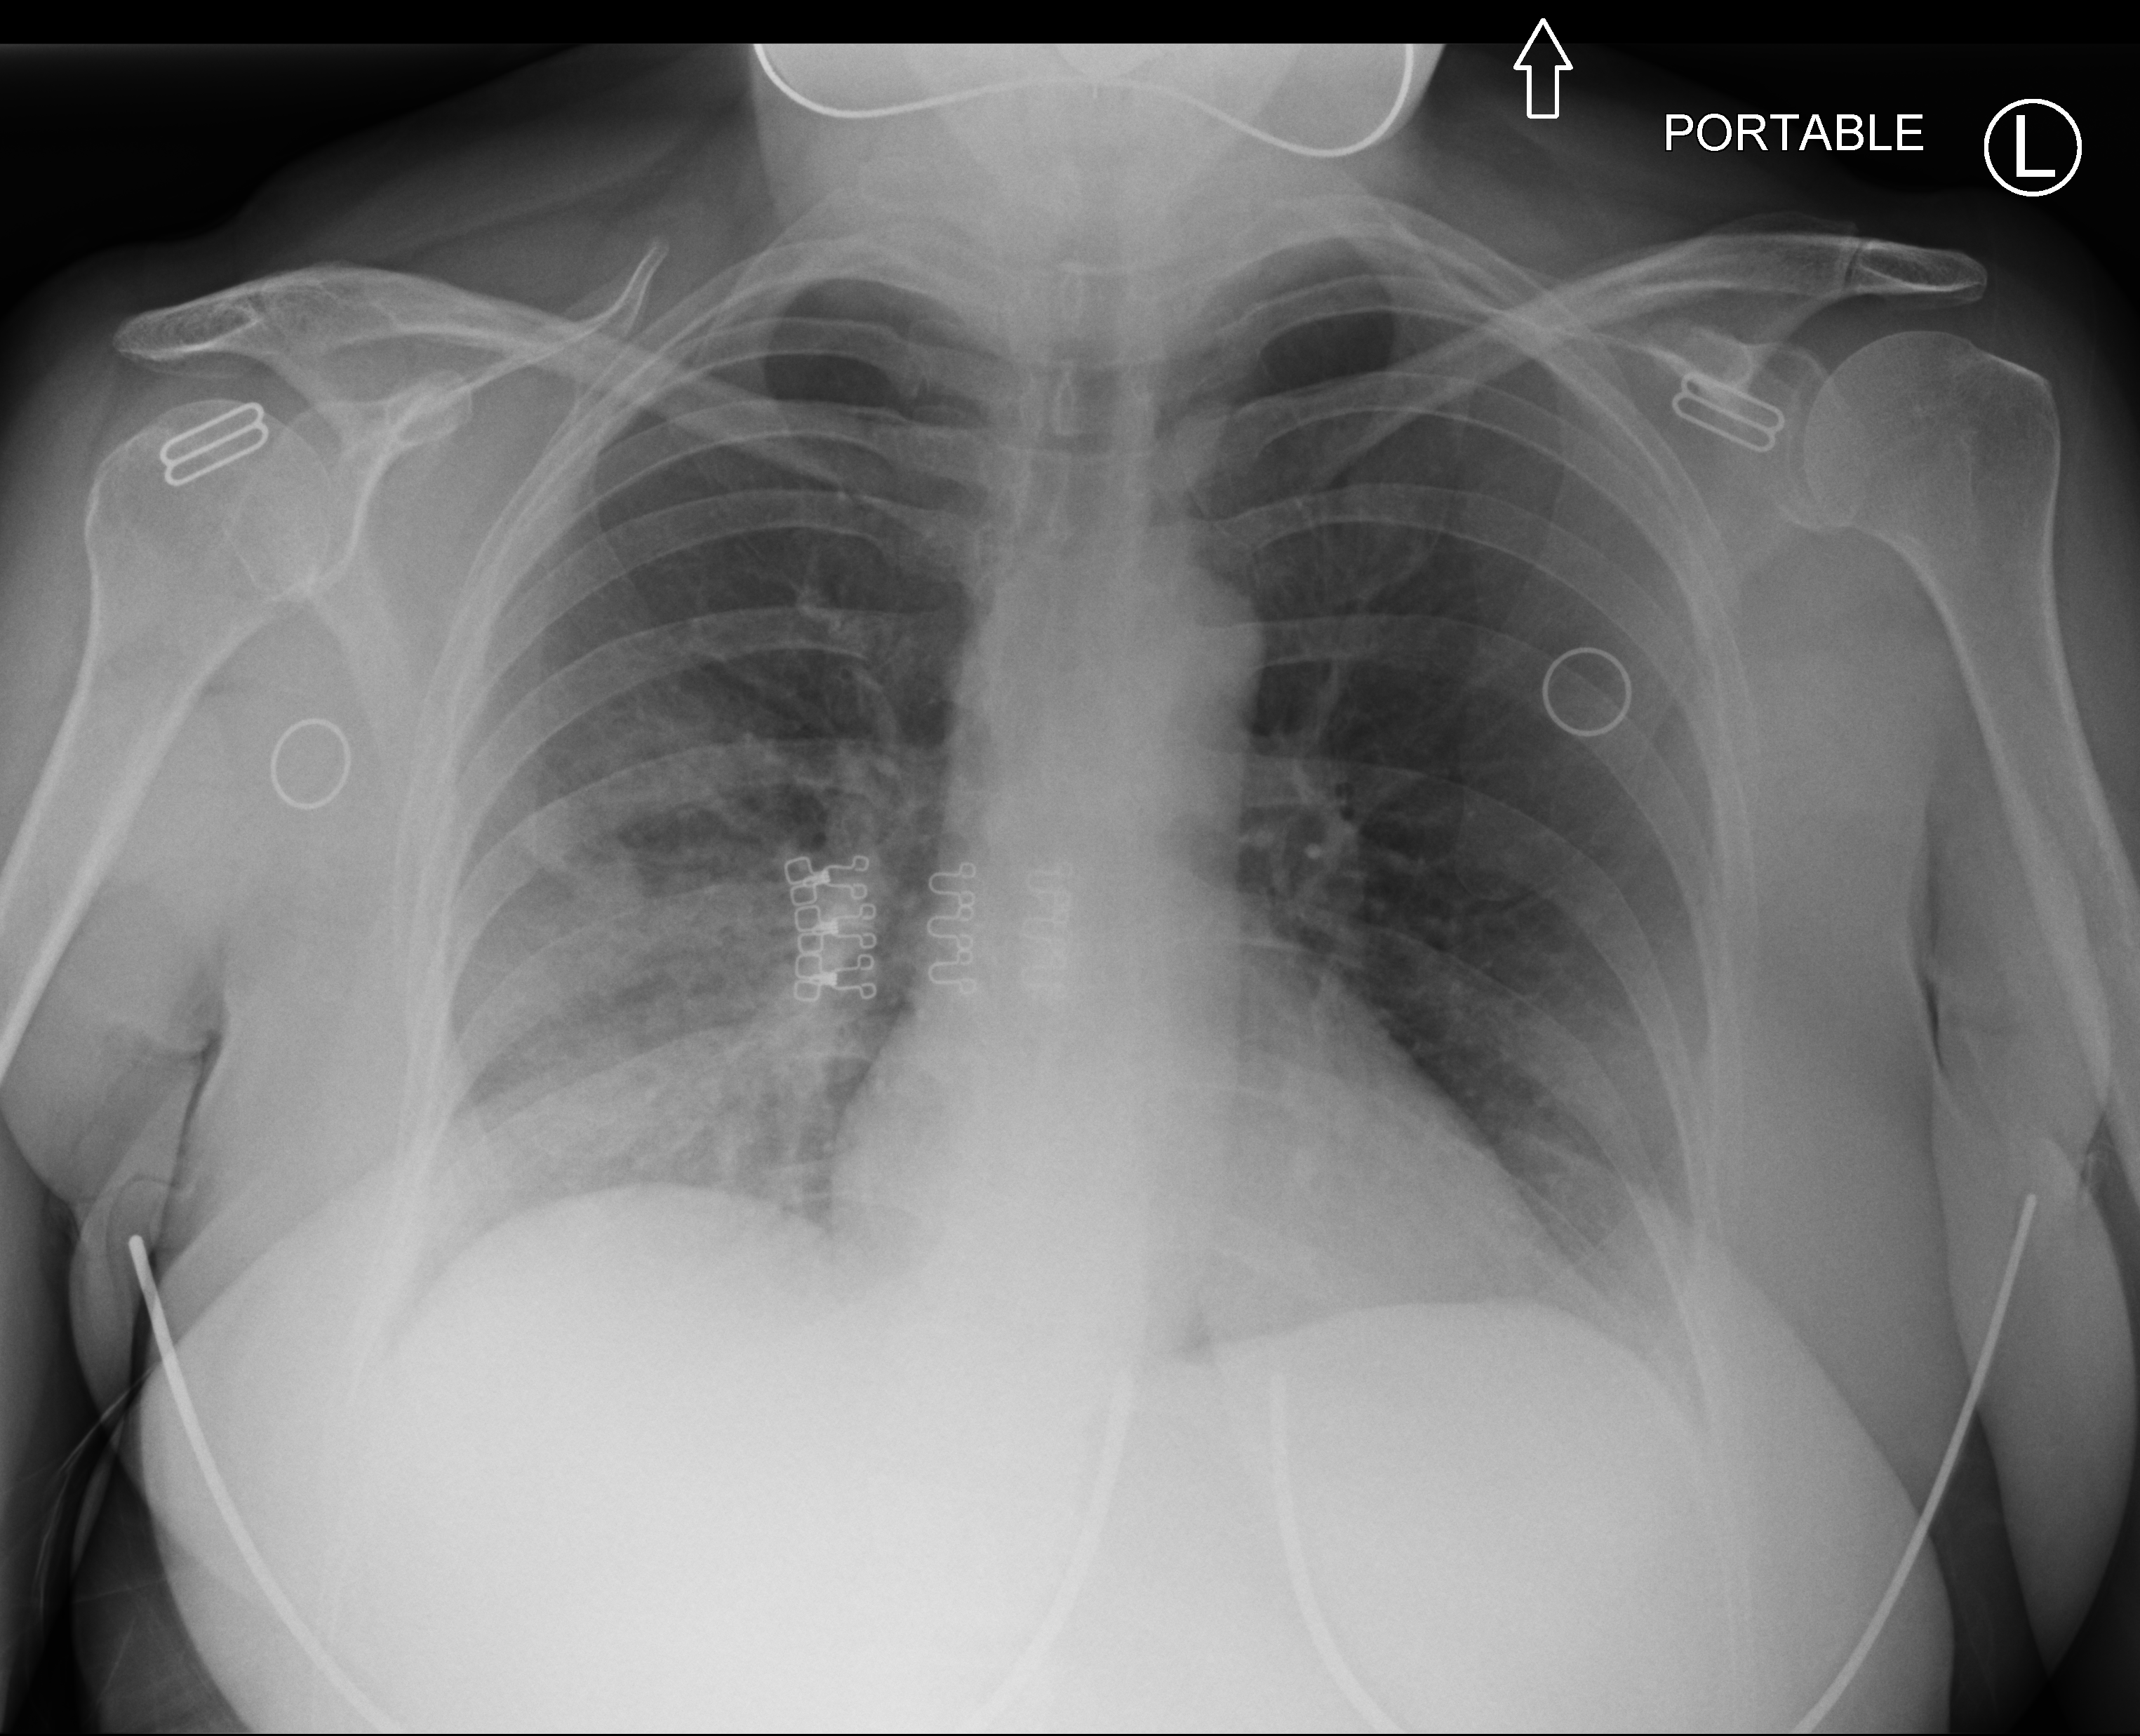
Chest X-ray (portable), anteroposterior (AP) projection. Female patient hospitalised with COVID-19, age 18–59 years.
Admission-level facts for this patient (not findings on this image; timing relative to this image not recorded): mechanically ventilated during this hospital stay: no.